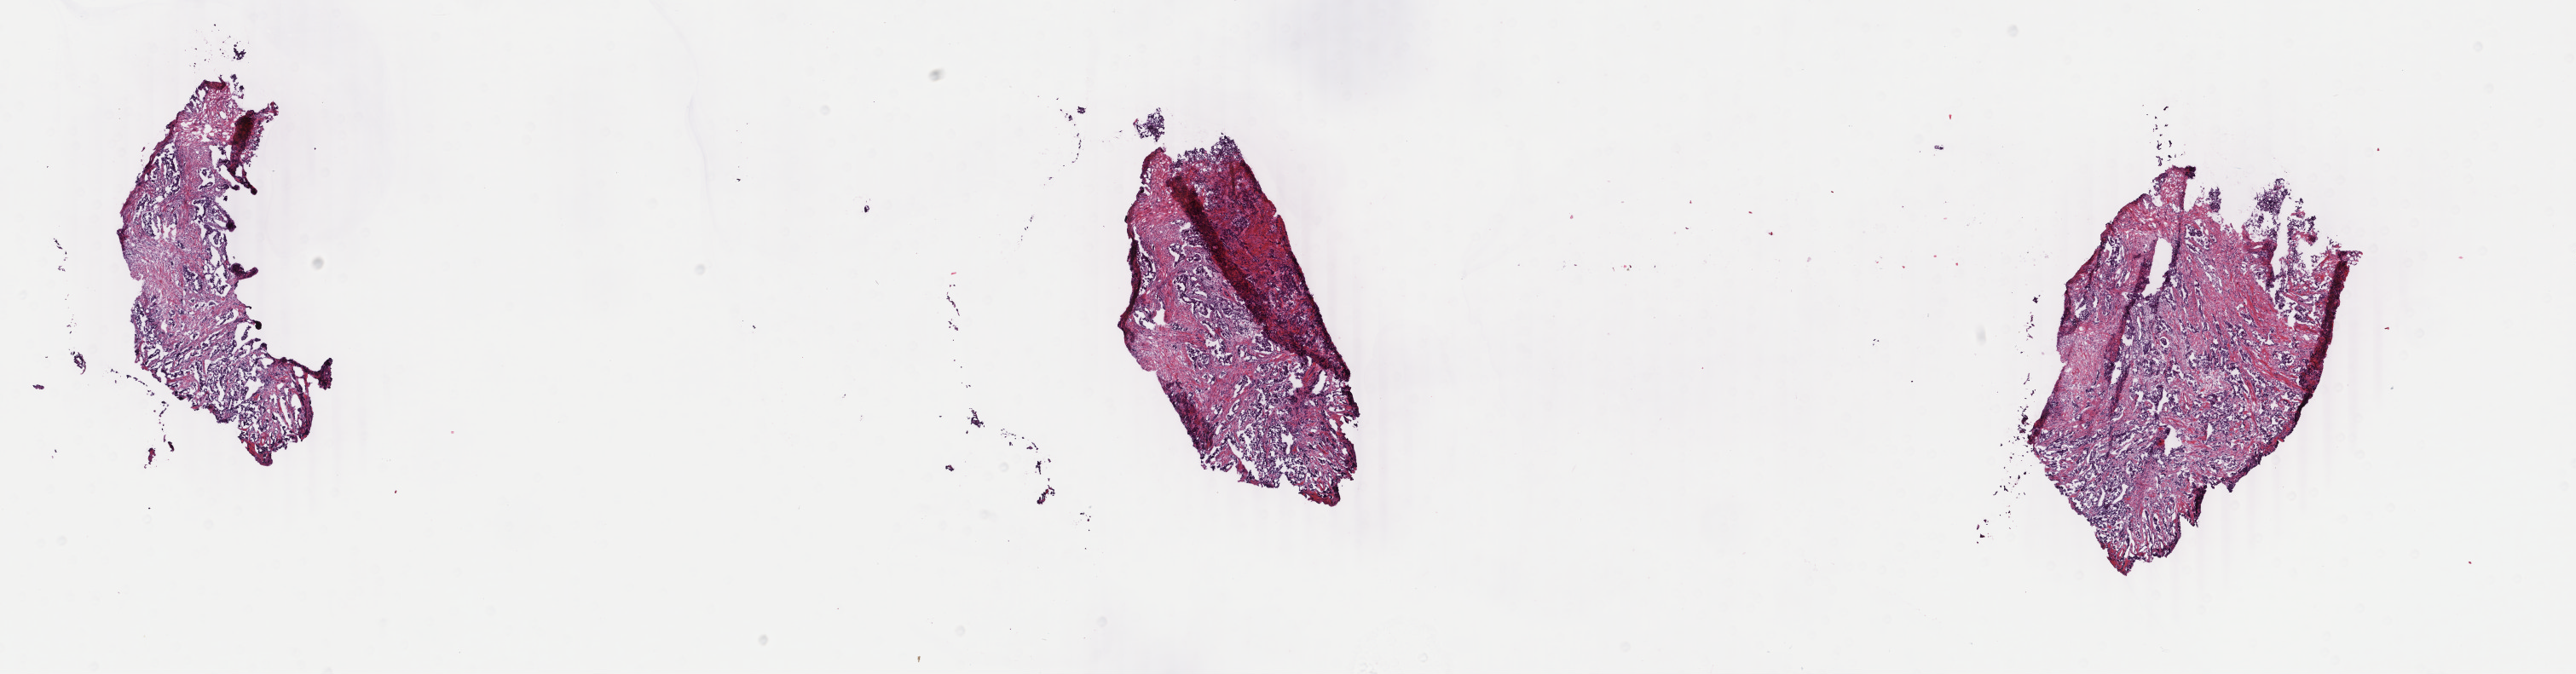
Whole-slide histology image, H&E, shown as a low-resolution overview of the whole scanned area (about 24.0 x 6.3 mm, slide scanned at 40x). Frozen section. Primary tumour sample from the breast. Patient: female, age at initial diagnosis 62 years. Slide review estimates, as recorded: tumour cells 80%, tumour nuclei 80%, normal cells 0%, stromal cells 20%, necrosis 0%. Inflammatory infiltration, as recorded: lymphocyte infiltration 1%, monocyte infiltration 0%, neutrophil infiltration 0%.
- histologic diagnosis: Infiltrating duct carcinoma, NOS
- laterality: left
- AJCC pathologic stage: IV